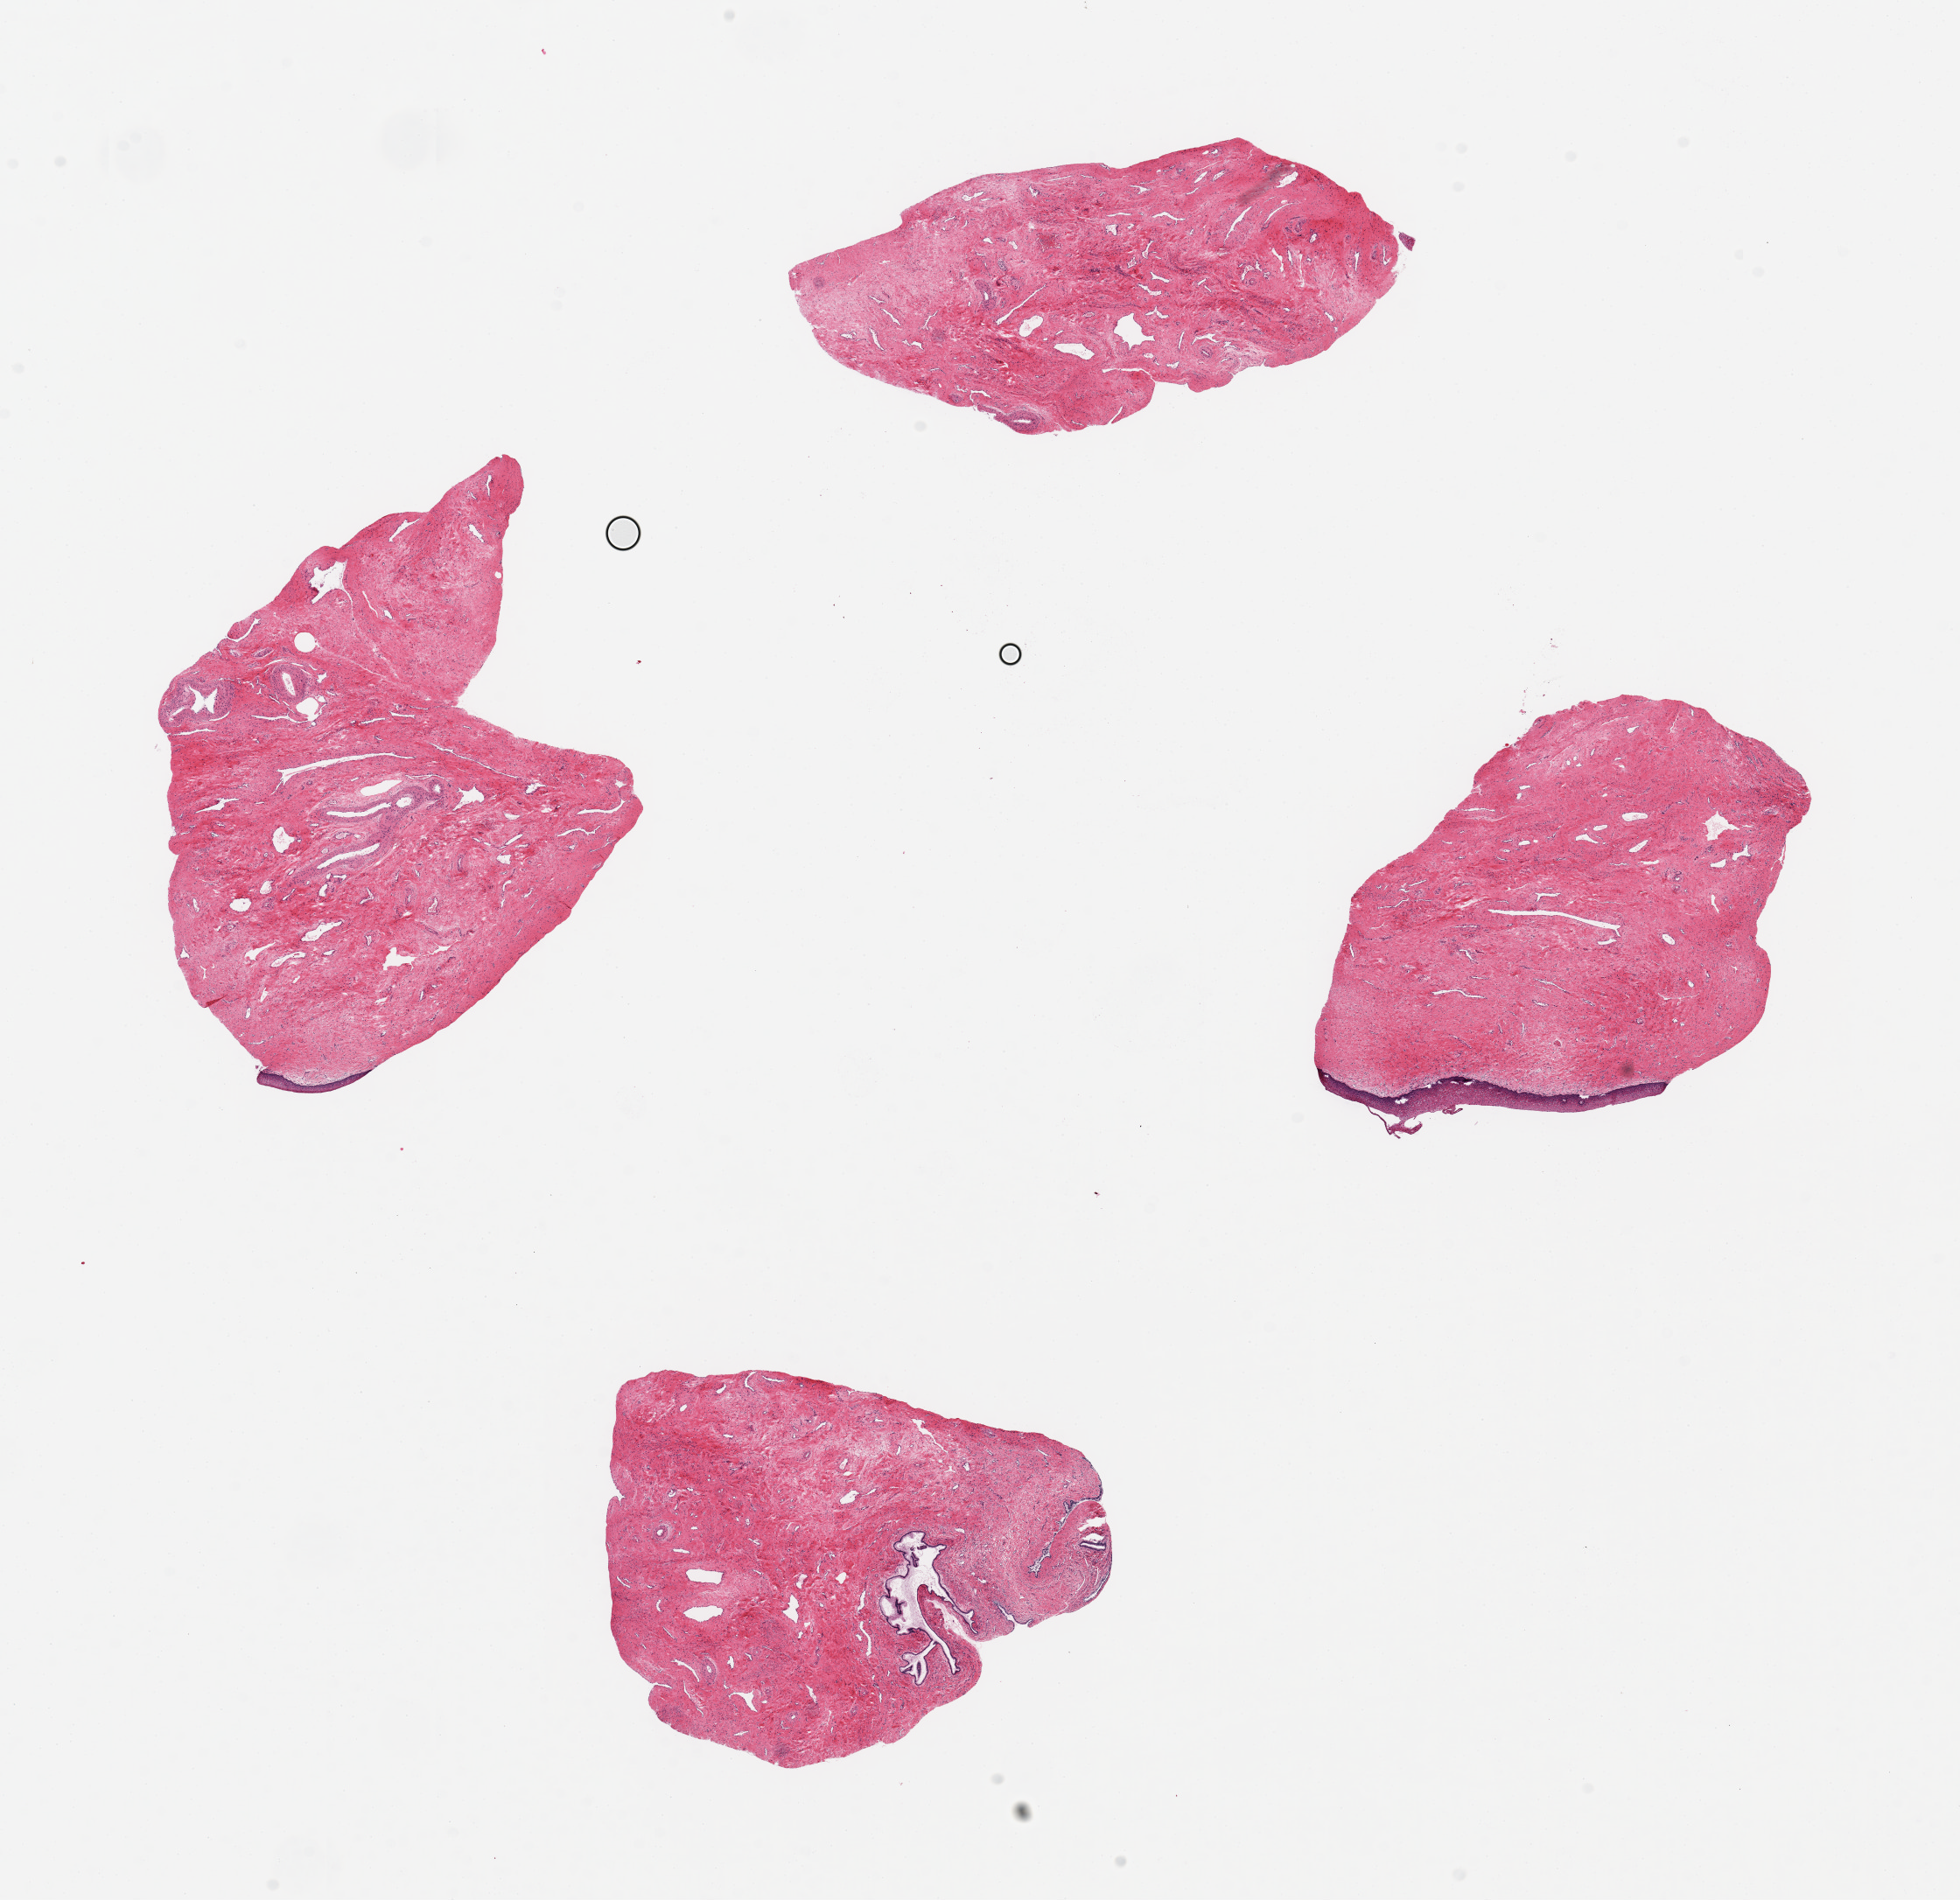
Whole-slide image, hematoxylin and eosin (H&E) stain — whole scanned area (about 17.7 x 17.2 mm) shown as a low-resolution overview. PAXgene-fixed, paraffin-embedded tissue. Target tissue: exocervix. Donor tissue sample. Donor sex: female.
Reviewer comment on this tissue sample: 4 pieces, ~4x4mm; Only one with significant ectocervical squamous mucosa, ~5% of thickness.